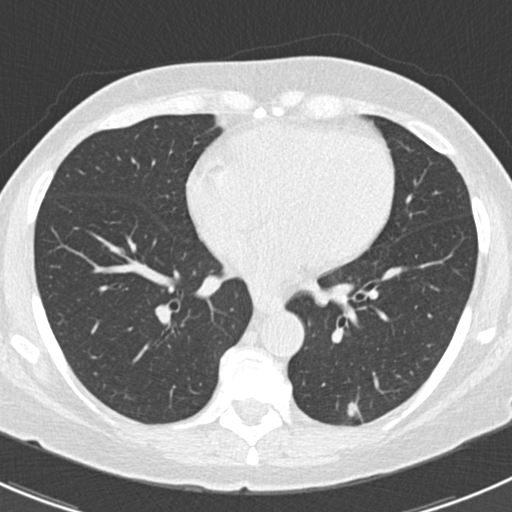
Low-dose screening chest CT, one axial slice. Position 79 of 166 along the scan axis. Reconstruction kernel B30f. Lung window (W 1500 / L -600 HU). 512 × 512 image matrix.
Annotated regions visible in this slice (expert manual segmentation):
- lesion 1 (tumor, lower lobe of left lung): bounding box <347,402,359,416> (left, top, right, bottom; pixels)